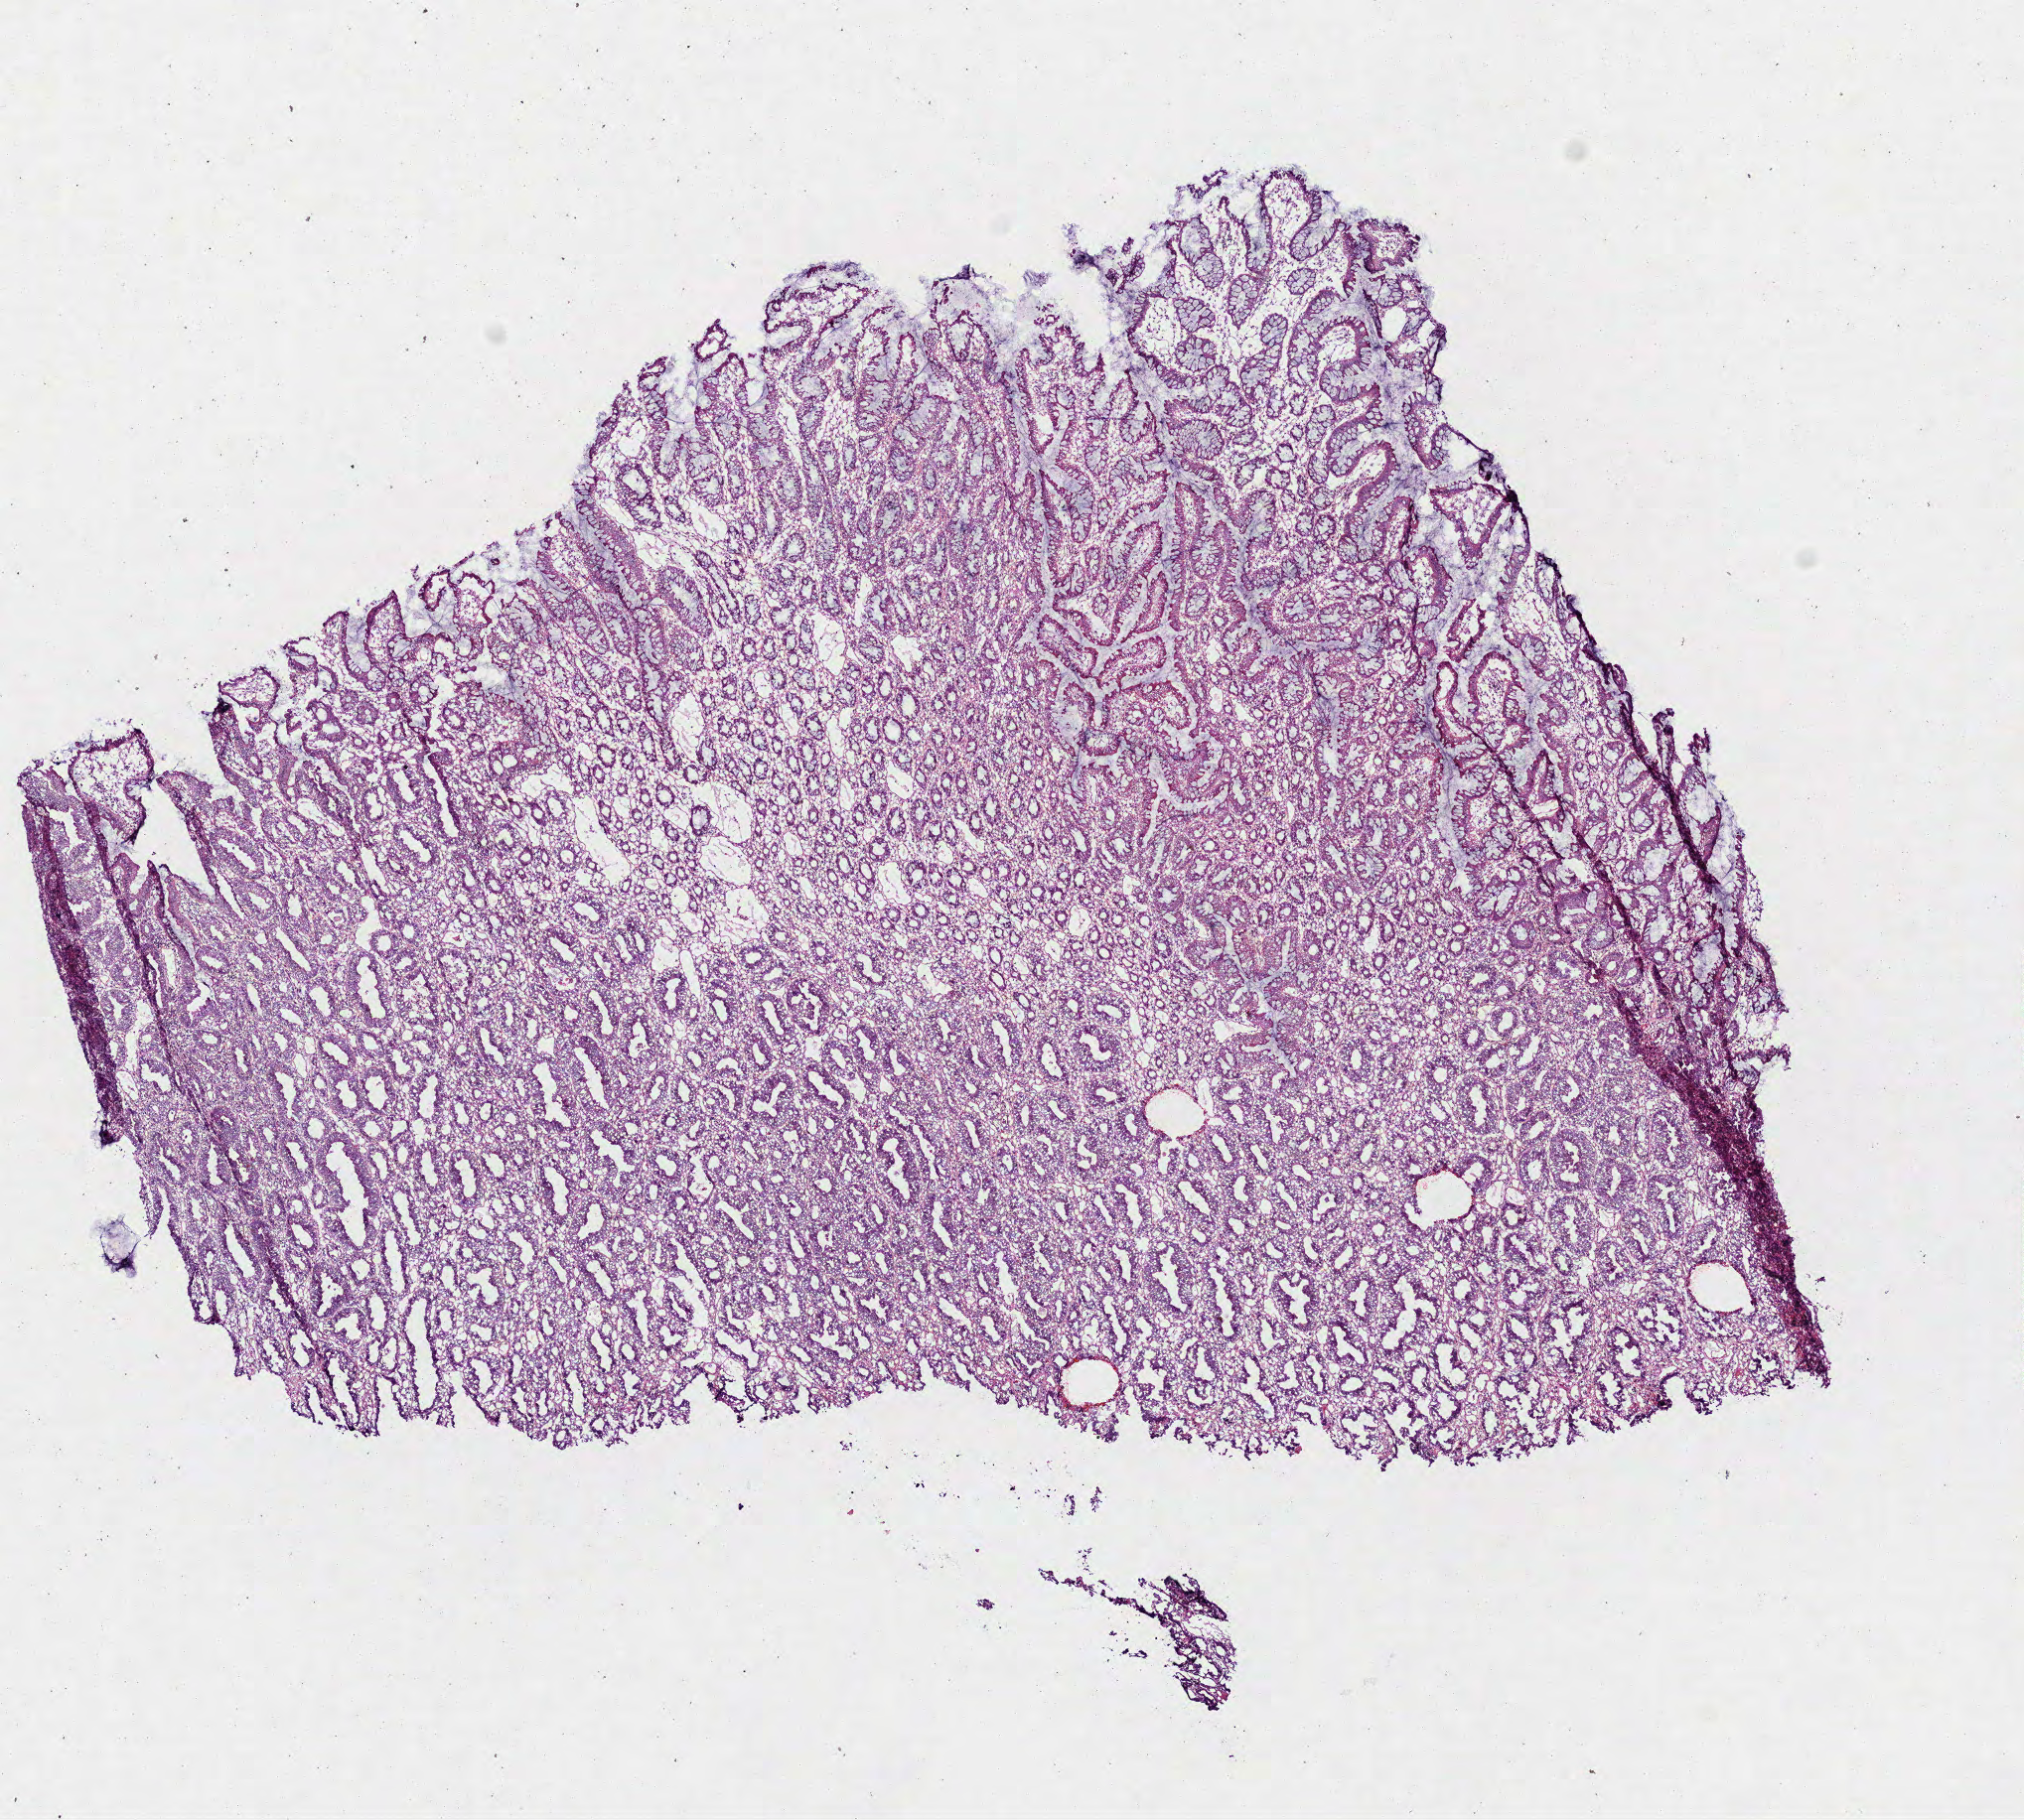
H&E whole-slide image, whole scanned area (about 8.2 x 7.4 mm, from a 40x scan) shown as a low-resolution overview, frozen section from the bottom of the tissue portion, primary tumour sample from the rectum. Male patient; age at initial diagnosis 60 years. Pathologist review of this section (percent, as recorded): tumour cells 55%, tumour nuclei 60%, normal cells 25%, stromal cells 20%, necrosis 0%.
Histologic diagnosis: Adenocarcinoma, NOS (rectosigmoid junction).